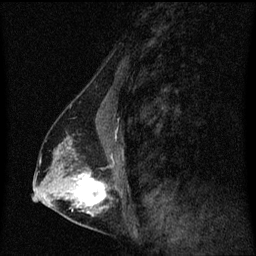
Breast MRI (dynamic contrast-enhanced), one sagittal slice; slice 33 of 60 in the series (ordered by position); dynamic contrast-enhanced series, image 2 of 3 at this slice position (ordered by acquisition); 1.5 T; TE 4.2 ms, TR 8.4 ms; 256 × 256 image matrix, field of view 200 × 200 mm. Female patient, age 40 years. From the clinical record (not read from this slice): setting: breast cancer imaged before/during neoadjuvant chemotherapy; receptor status: triple-negative.
Annotated regions visible in this slice (semi-automatically segmented with operator editing):
- analysis volume of interest (the breast-tissue region the enhancement analysis was run in; not a lesion): box from (x=44, y=128) to (x=117, y=221) px
- tumour enhancement mask (voxels above the 70 % enhancement threshold inside the analysis volume of interest): (x=75, y=174)–(x=107, y=213)